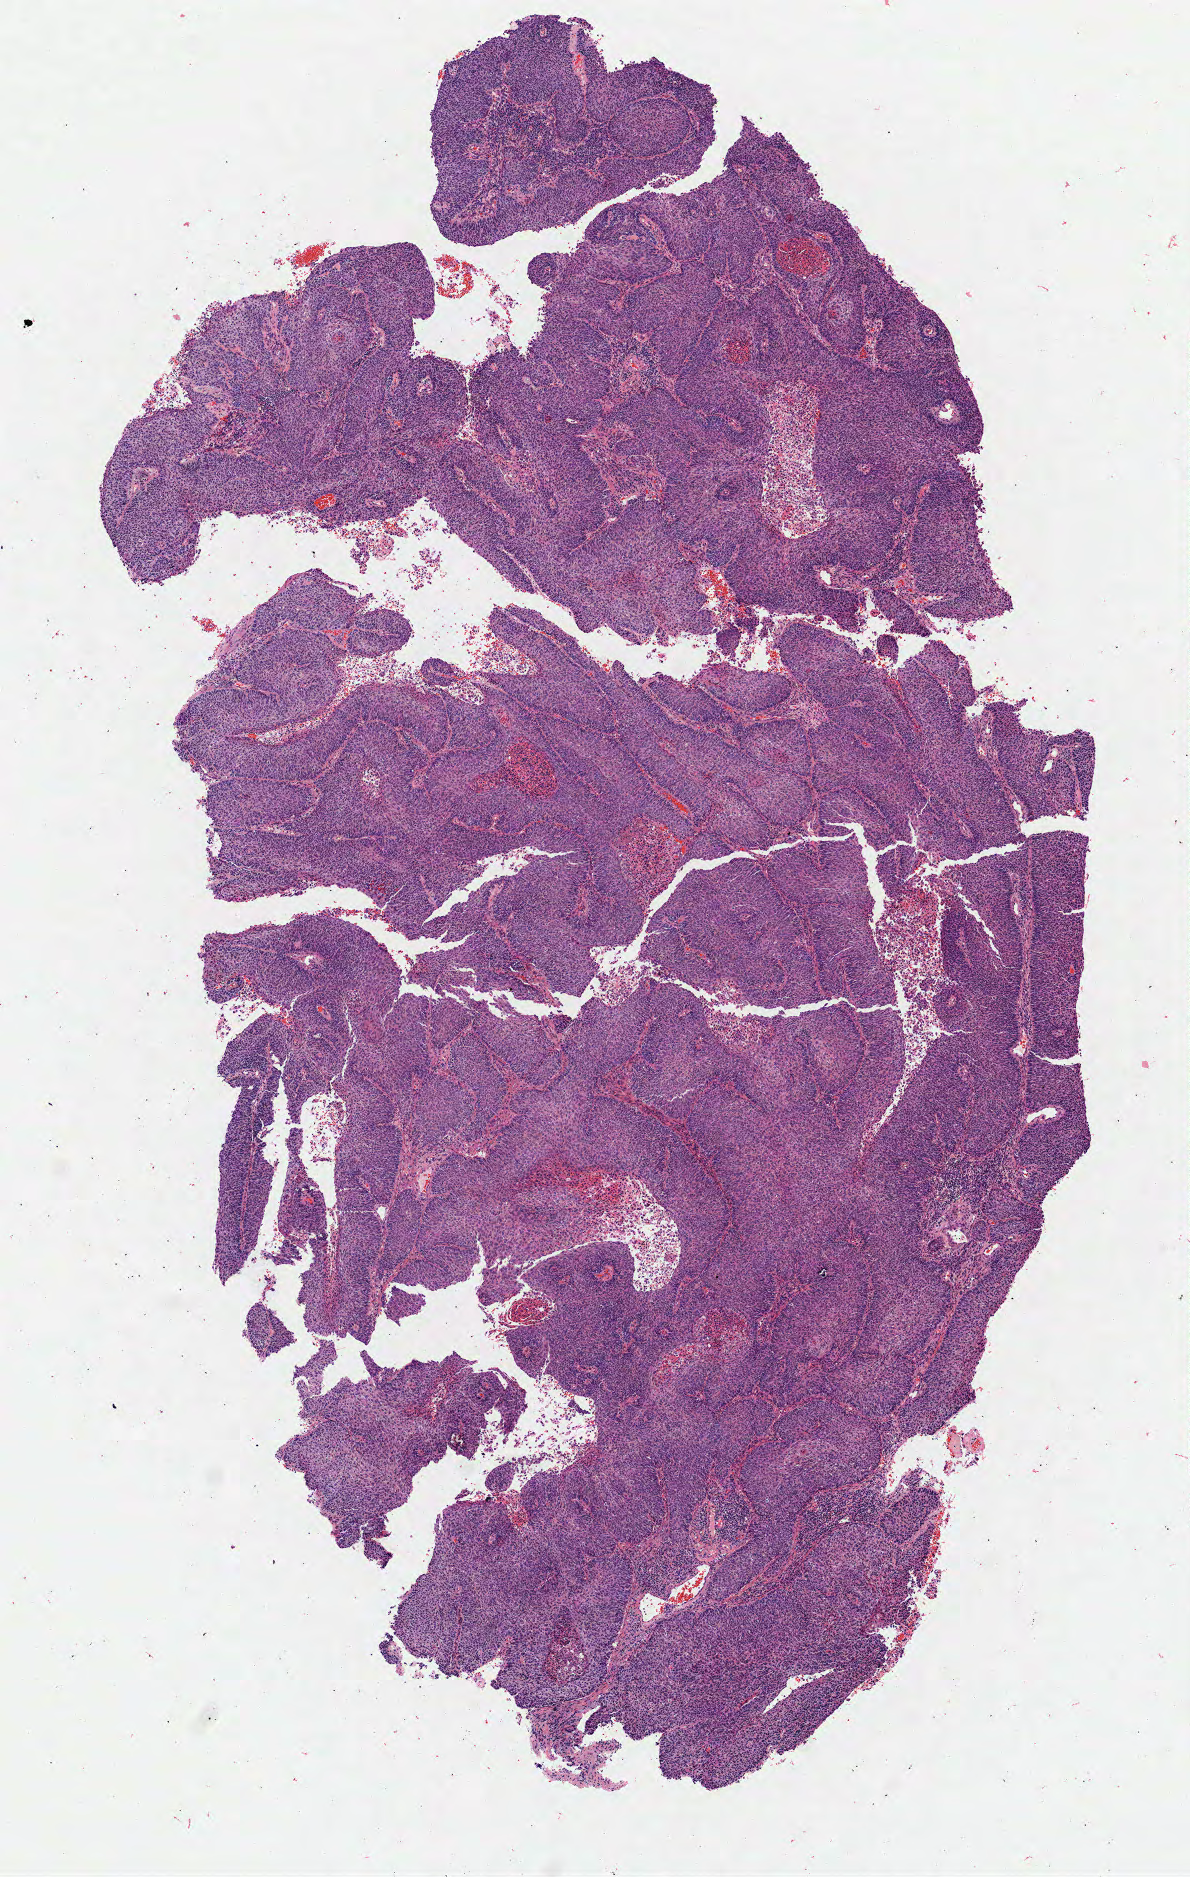
Digitized haematoxylin and eosin-stained section — a low-resolution overview of the entire scanned area, about 4.7 x 7.5 mm; tumor tissue; anatomic site: cervix. Female patient, aged 56.
- diagnosis: Squamous cell carcinoma, large cell, nonkeratinizing, NOS